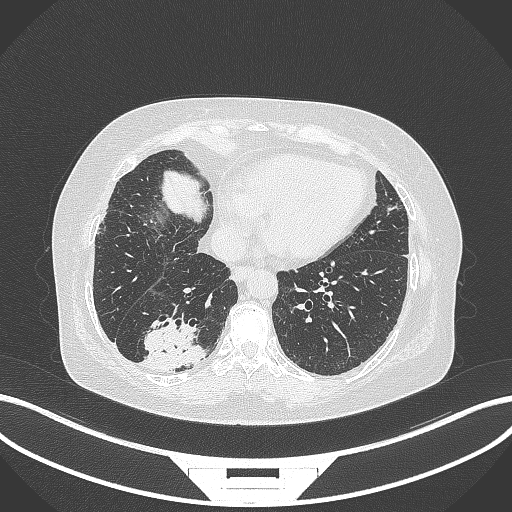
Chest CT, one axial slice. Slice 68 of 296 in the series (ordered by position). Reconstruction kernel B70f. 120 kVp. Lung window (W 1500 / L -600 HU). 1 mm slice thickness. 512 × 512 image matrix. Female patient, age 65 years. Case-level facts recorded for this patient, not image findings: clinical TNM (as recorded): T2b N1 M0; histopathological grade: G1.
Annotated regions visible in this slice (rectangle marked by the reading radiologist):
- lung tumour (recorded histology: adenocarcinoma): bounding box <138,314,209,373> (left, top, right, bottom; pixels)